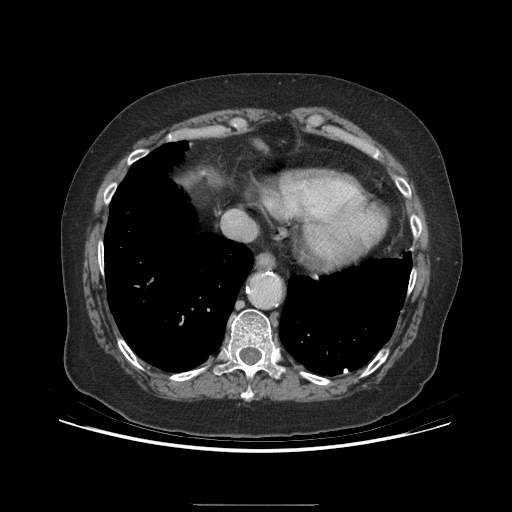
Contrast-enhanced abdominal CT (liver protocol), one axial slice; slice 182 of 192 in the series (ordered by position); reconstruction kernel STANDARD; soft-tissue window (W 400 / L 40 HU); 2.5 mm slice thickness; 512 × 512 image matrix, field of view 400 × 400 mm. Case-level facts recorded for this patient, not image findings: diagnosis: hepatocellular carcinoma (patient treated with transarterial chemoembolisation; whether this scan precedes or follows treatment is not stated here); TNM stage (as recorded): Stage-I; Child-Pugh class: A; tumour differentiation: moderately differentiated; tumour nodularity: uninodular.
Outlined on this slice (semi-automatically segmented with operator editing):
- abdominal aorta: bounding box <251,274,280,306> (left, top, right, bottom; pixels)